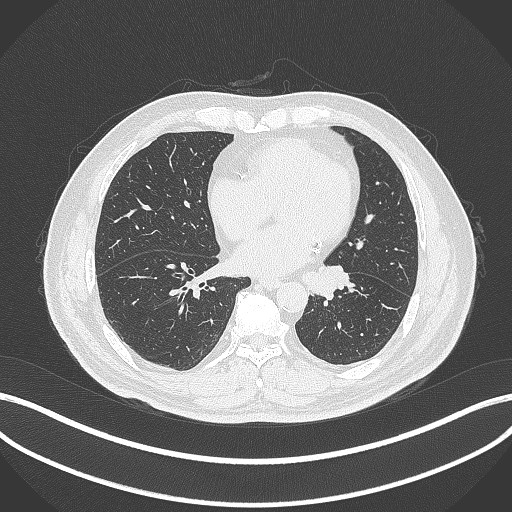
Chest CT, one axial slice; position 109 of 312 along the scan axis; reconstruction kernel B70f; lung window (W 1500 / L -600 HU); 1 mm slice thickness; 512 × 512 image matrix, field of view 400 × 400 mm. Patient: male, 71 years. From the clinical record (not read from this slice): clinical TNM (as recorded): T1b N0 M0.
Structures marked on this image (rectangle marked by the reading radiologist):
- lung tumour (recorded histology: squamous cell carcinoma): bounding box <300,265,355,304> (left, top, right, bottom; pixels)